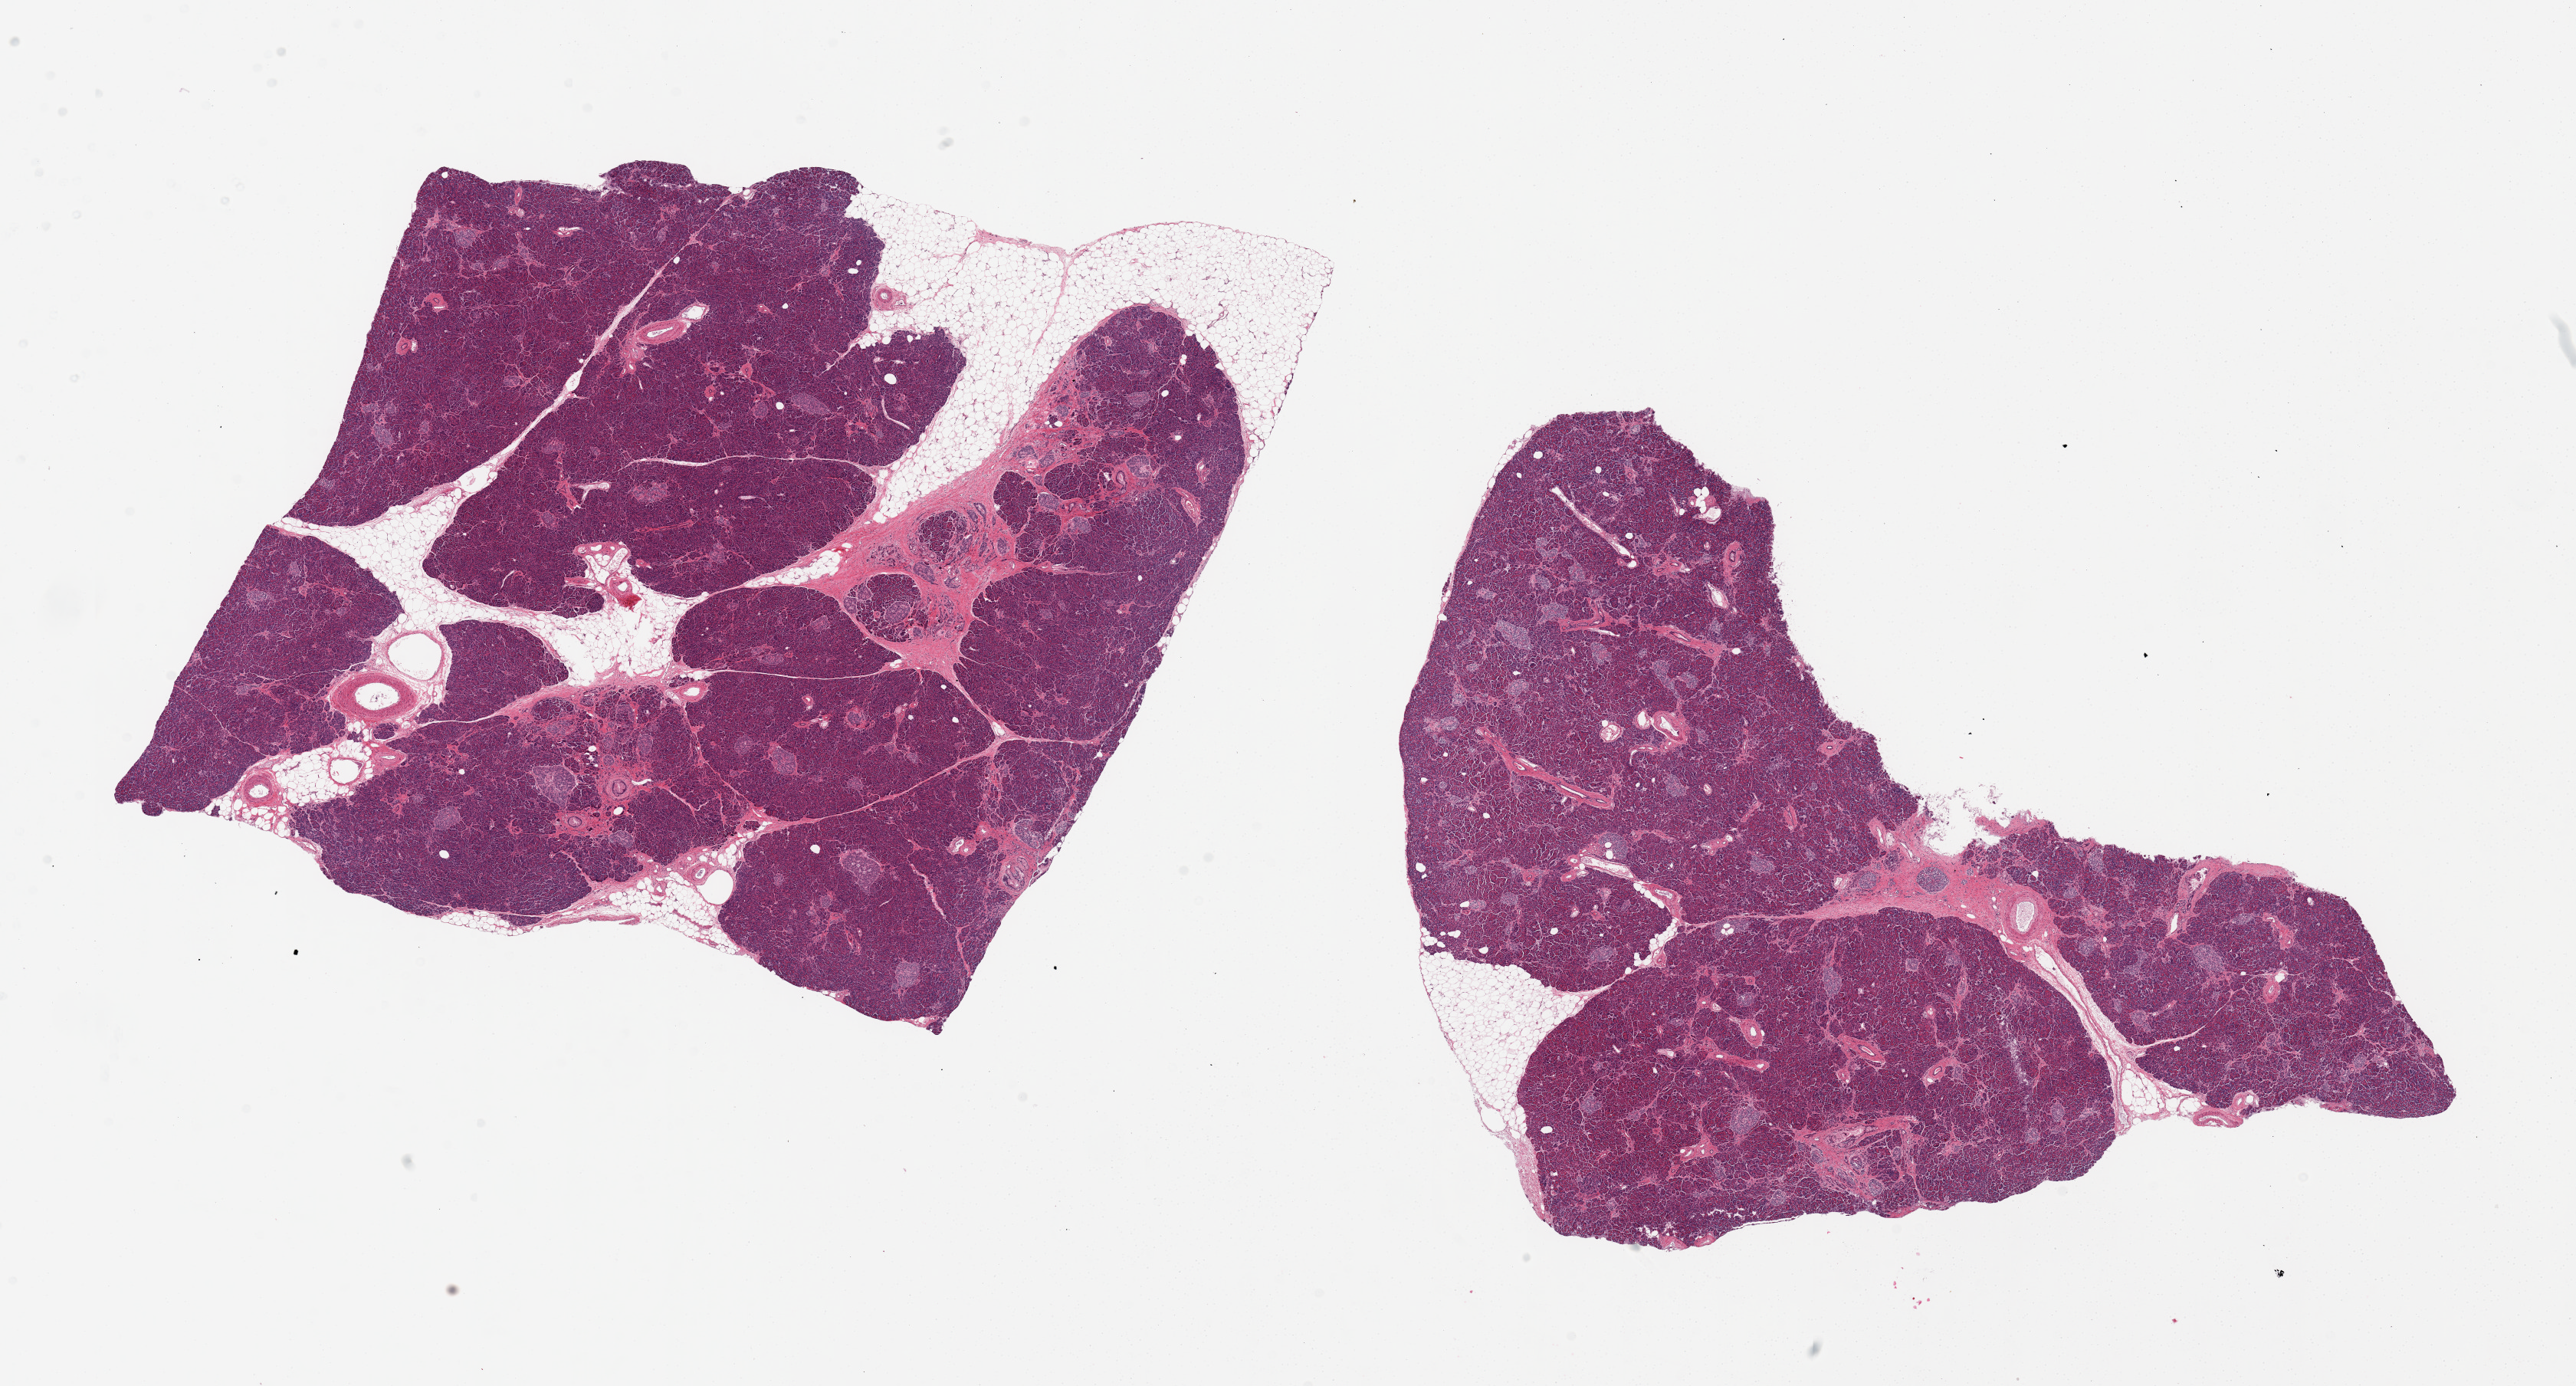
Whole-slide image, haematoxylin and eosin stain — low-resolution overview of the scanned area, about 26.6 x 14.3 mm; PAXgene-fixed, paraffin-embedded tissue; target tissue: pancreas; tissue donor sample. Male donor.
Review note (as recorded): 2 pieces; approximately 10% fat (internal and attached).